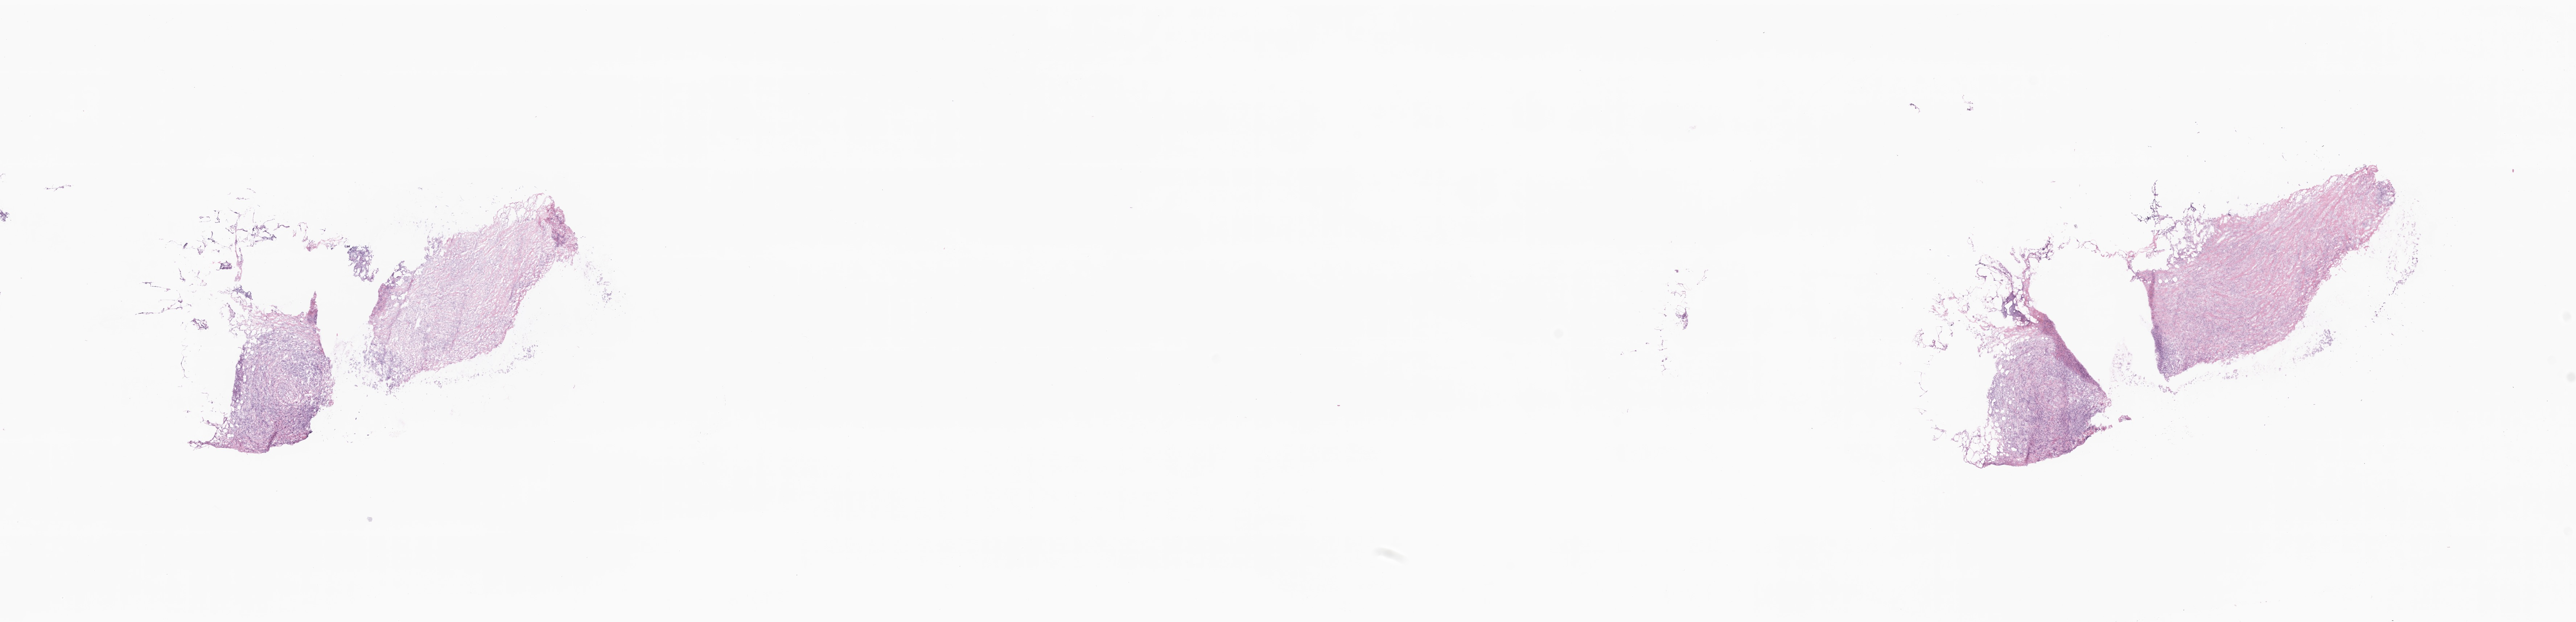
Whole-slide image, haematoxylin and eosin stain, whole scanned area (about 29.9 x 7.2 mm) shown as a low-resolution overview; cryosection; primary tumor; anatomic site: breast. Female patient; age at initial diagnosis 58 years. Pathologist review of this section (percent, as recorded): tumor cells 95%, tumor nuclei 90%, stromal cells 0%, necrosis 0%, normal cells 5%. Inflammatory infiltration, as recorded: lymphocyte infiltration 0%, monocyte infiltration 0%, neutrophil infiltration 0%.
Diagnosis: Infiltrating duct carcinoma, NOS. Section: top of the tissue portion.